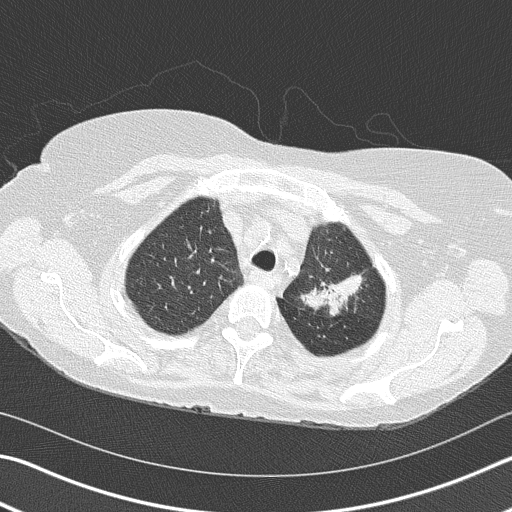
Axial slice from a low-dose chest CT screening exam. Second annual screen. Lung window (W 1500 / L -600 HU). Lung (sharp) reconstruction kernel (B50f). 120 kVp. 512 × 512 image matrix, field of view 342 × 342 mm. Female, age 68 years at enrolment.
Expert reader's lesion annotation, bounding box [x1, y1, x2, y2] px = [290, 233, 374, 324]. Reader record for this screening exam (exam-level; its link to the box is not recorded): non-calcified nodule or mass ≥4 mm, left upper lobe, 4 × 2 mm, spiculated (stellate) margins, soft tissue attenuation, pre-existing on the prior screen: yes; interval growth: yes. Official screen result: positive, other. Later outcome: lung cancer diagnosed 392 days after this screen — adenocarcinoma, NOS, left upper lobe, poorly differentiated (G3), stage IB (AJCC 6th edition), 50 mm at pathology.